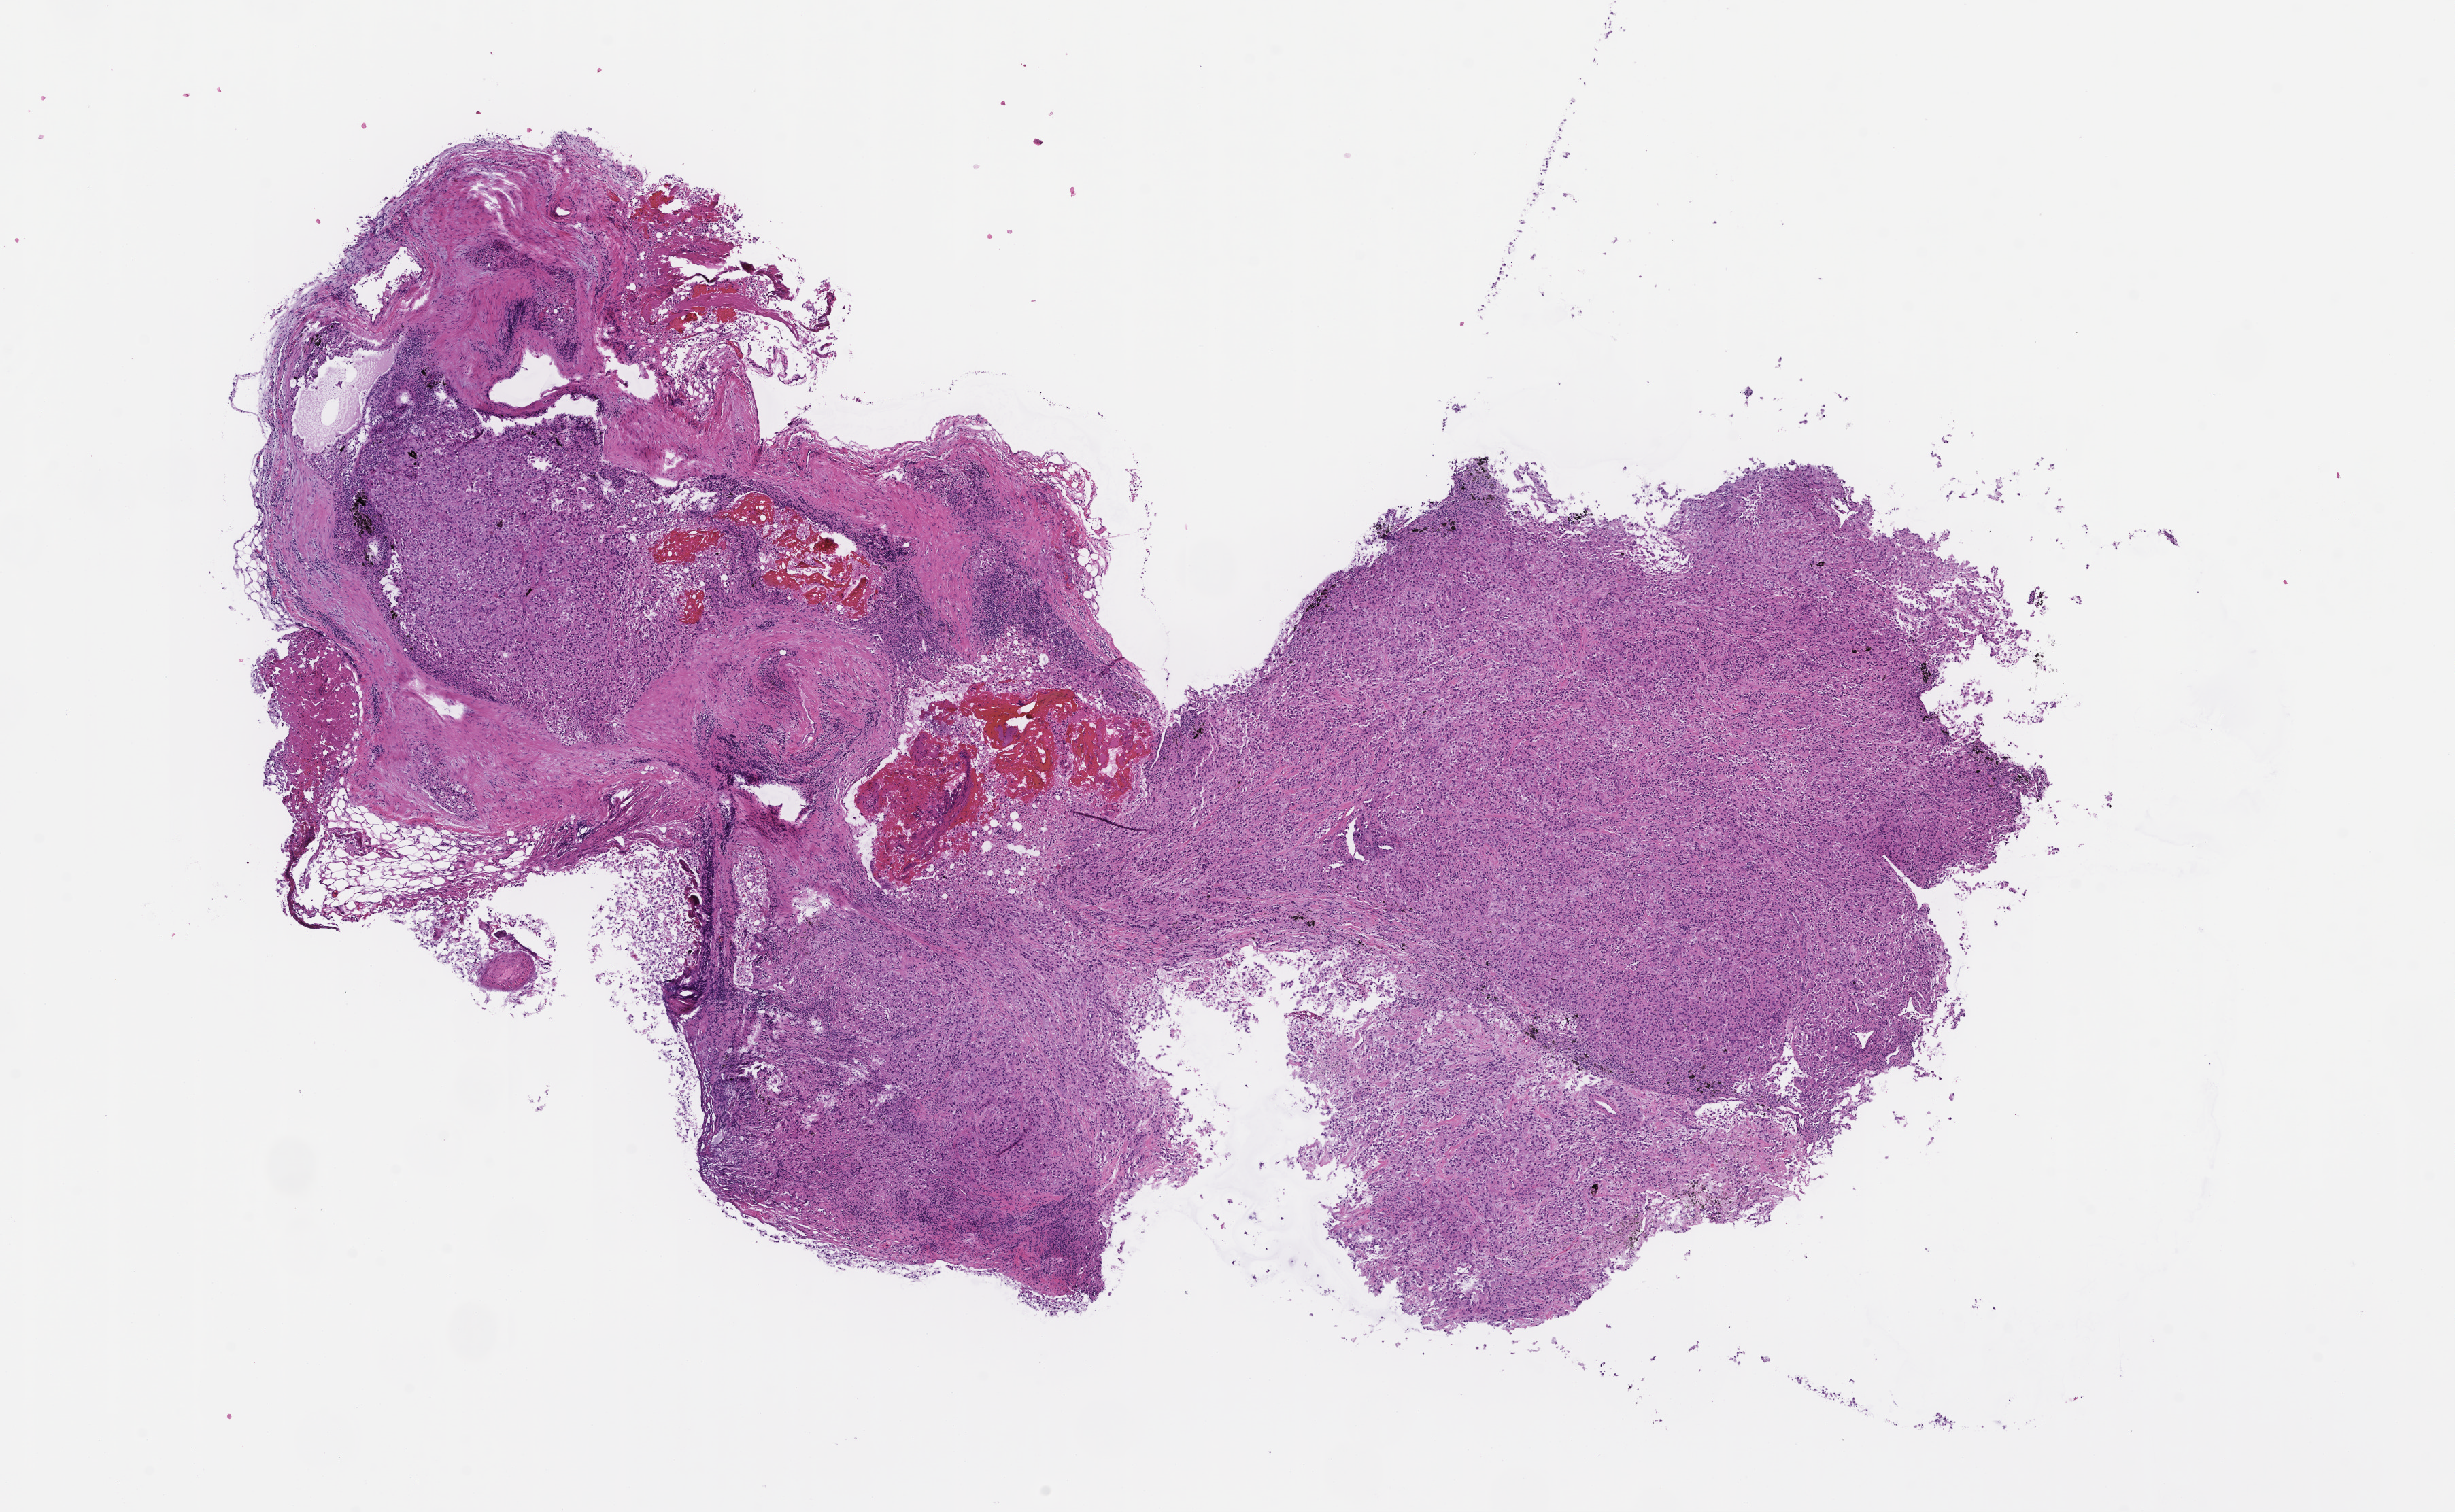
Digitized haematoxylin and eosin-stained section — a low-resolution overview of the entire scanned area, about 14.6 x 9.0 mm. Formalin-fixed, paraffin-embedded (FFPE) tissue. Patient: female.
- this section: metastasis (sampled organ not recorded)
- primary diagnosis of the patient: Non-Small Cell Lung Carcinoma